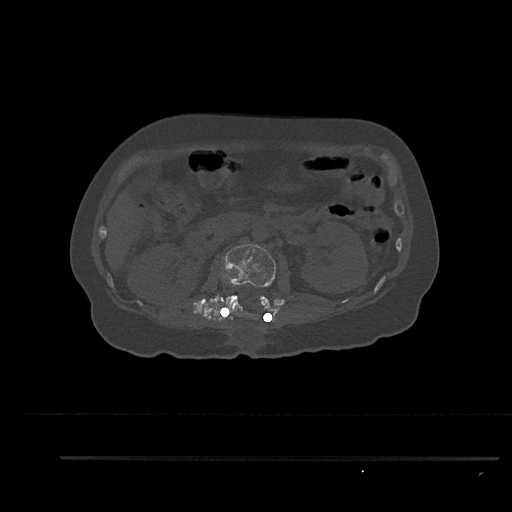
CT including the spine, one axial slice. Position 184 of 797 along the scan axis. Reconstruction kernel Br40s/3. 120 kVp. Bone window (W 1800 / L 400 HU). 0.5 mm slice thickness. 512 × 512 image matrix, field of view 408 × 408 mm. Patient: female, 44 years. Case-level facts recorded for this patient, not image findings: primary cancer: renal.
Outlined on this slice (semi-automatically segmented with operator editing):
- L1 vertebra: bounding box (x1, y1, x2, y2) in pixels: (233, 285, 239, 308)
- L2 vertebra: (224, 244, 276, 320)